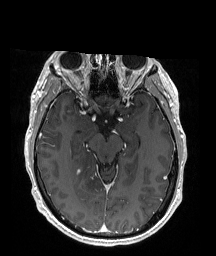
Brain MRI from a brain-tumour surgery series, one axial slice; T1-weighted post-contrast; 1 mm slice thickness; 216 × 256 image matrix. Case-level facts recorded for this patient, not image findings: histopathology: Oligodendroglioma; WHO grade: 2; IDH mutation: yes; tumour location: Right Parietal.
Outlined on this slice (manually delineated by an expert):
- tumour: bounding box [x1, y1, x2, y2] px = [71, 150, 99, 205]